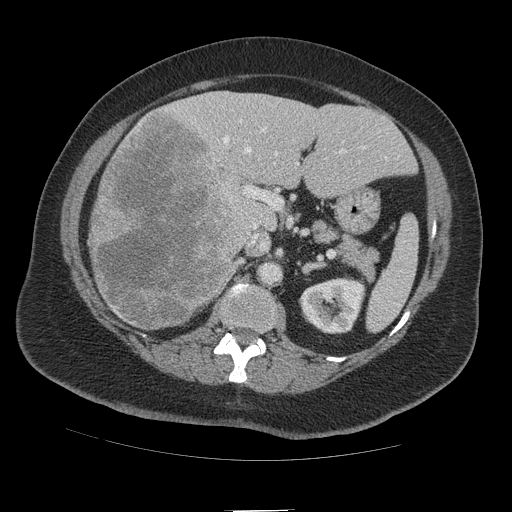
Contrast-enhanced abdominal CT (liver protocol), one axial slice. Slice 56 of 109 in the series (ordered by position). Reconstruction kernel STANDARD. Soft-tissue window (W 400 / L 40 HU). 2.5 mm slice thickness. 512 × 512 image matrix. From the clinical record (not read from this slice): diagnosis: hepatocellular carcinoma (patient treated with transarterial chemoembolisation; whether this scan precedes or follows treatment is not stated here); TNM stage (as recorded): Stage-IVB; Child-Pugh class: A; tumour nodularity: multinodular.
Annotated regions visible in this slice (semi-automatic segmentation, software-assisted and operator-edited):
- liver parenchyma outside the tumour (the mass and vessels are separate outlines, so this box may not span the whole liver): box from (x=88, y=90) to (x=412, y=330) px
- mass: (x=89, y=110)–(x=251, y=329)
- liver vessels: (x=174, y=109)–(x=387, y=247)